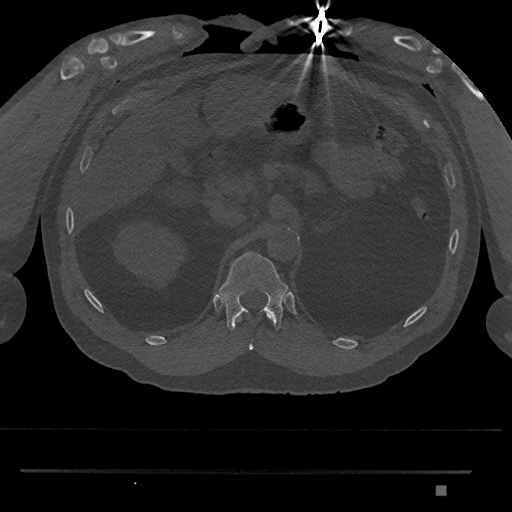
CT including the spine, one axial slice; slice 904 of 1134 in the series (ordered by position); reconstruction kernel Br40s/3; bone window (W 1800 / L 400 HU); 0.5 mm slice thickness; 512 × 512 image matrix. Patient: male, 65 years. From the clinical record (not read from this slice): primary cancer: prostate.
Structures marked on this image (semi-automatic segmentation, software-assisted and operator-edited):
- T11 vertebra: bounding box <237,312,272,350> (left, top, right, bottom; pixels)
- T12 vertebra: <219,251,288,331>